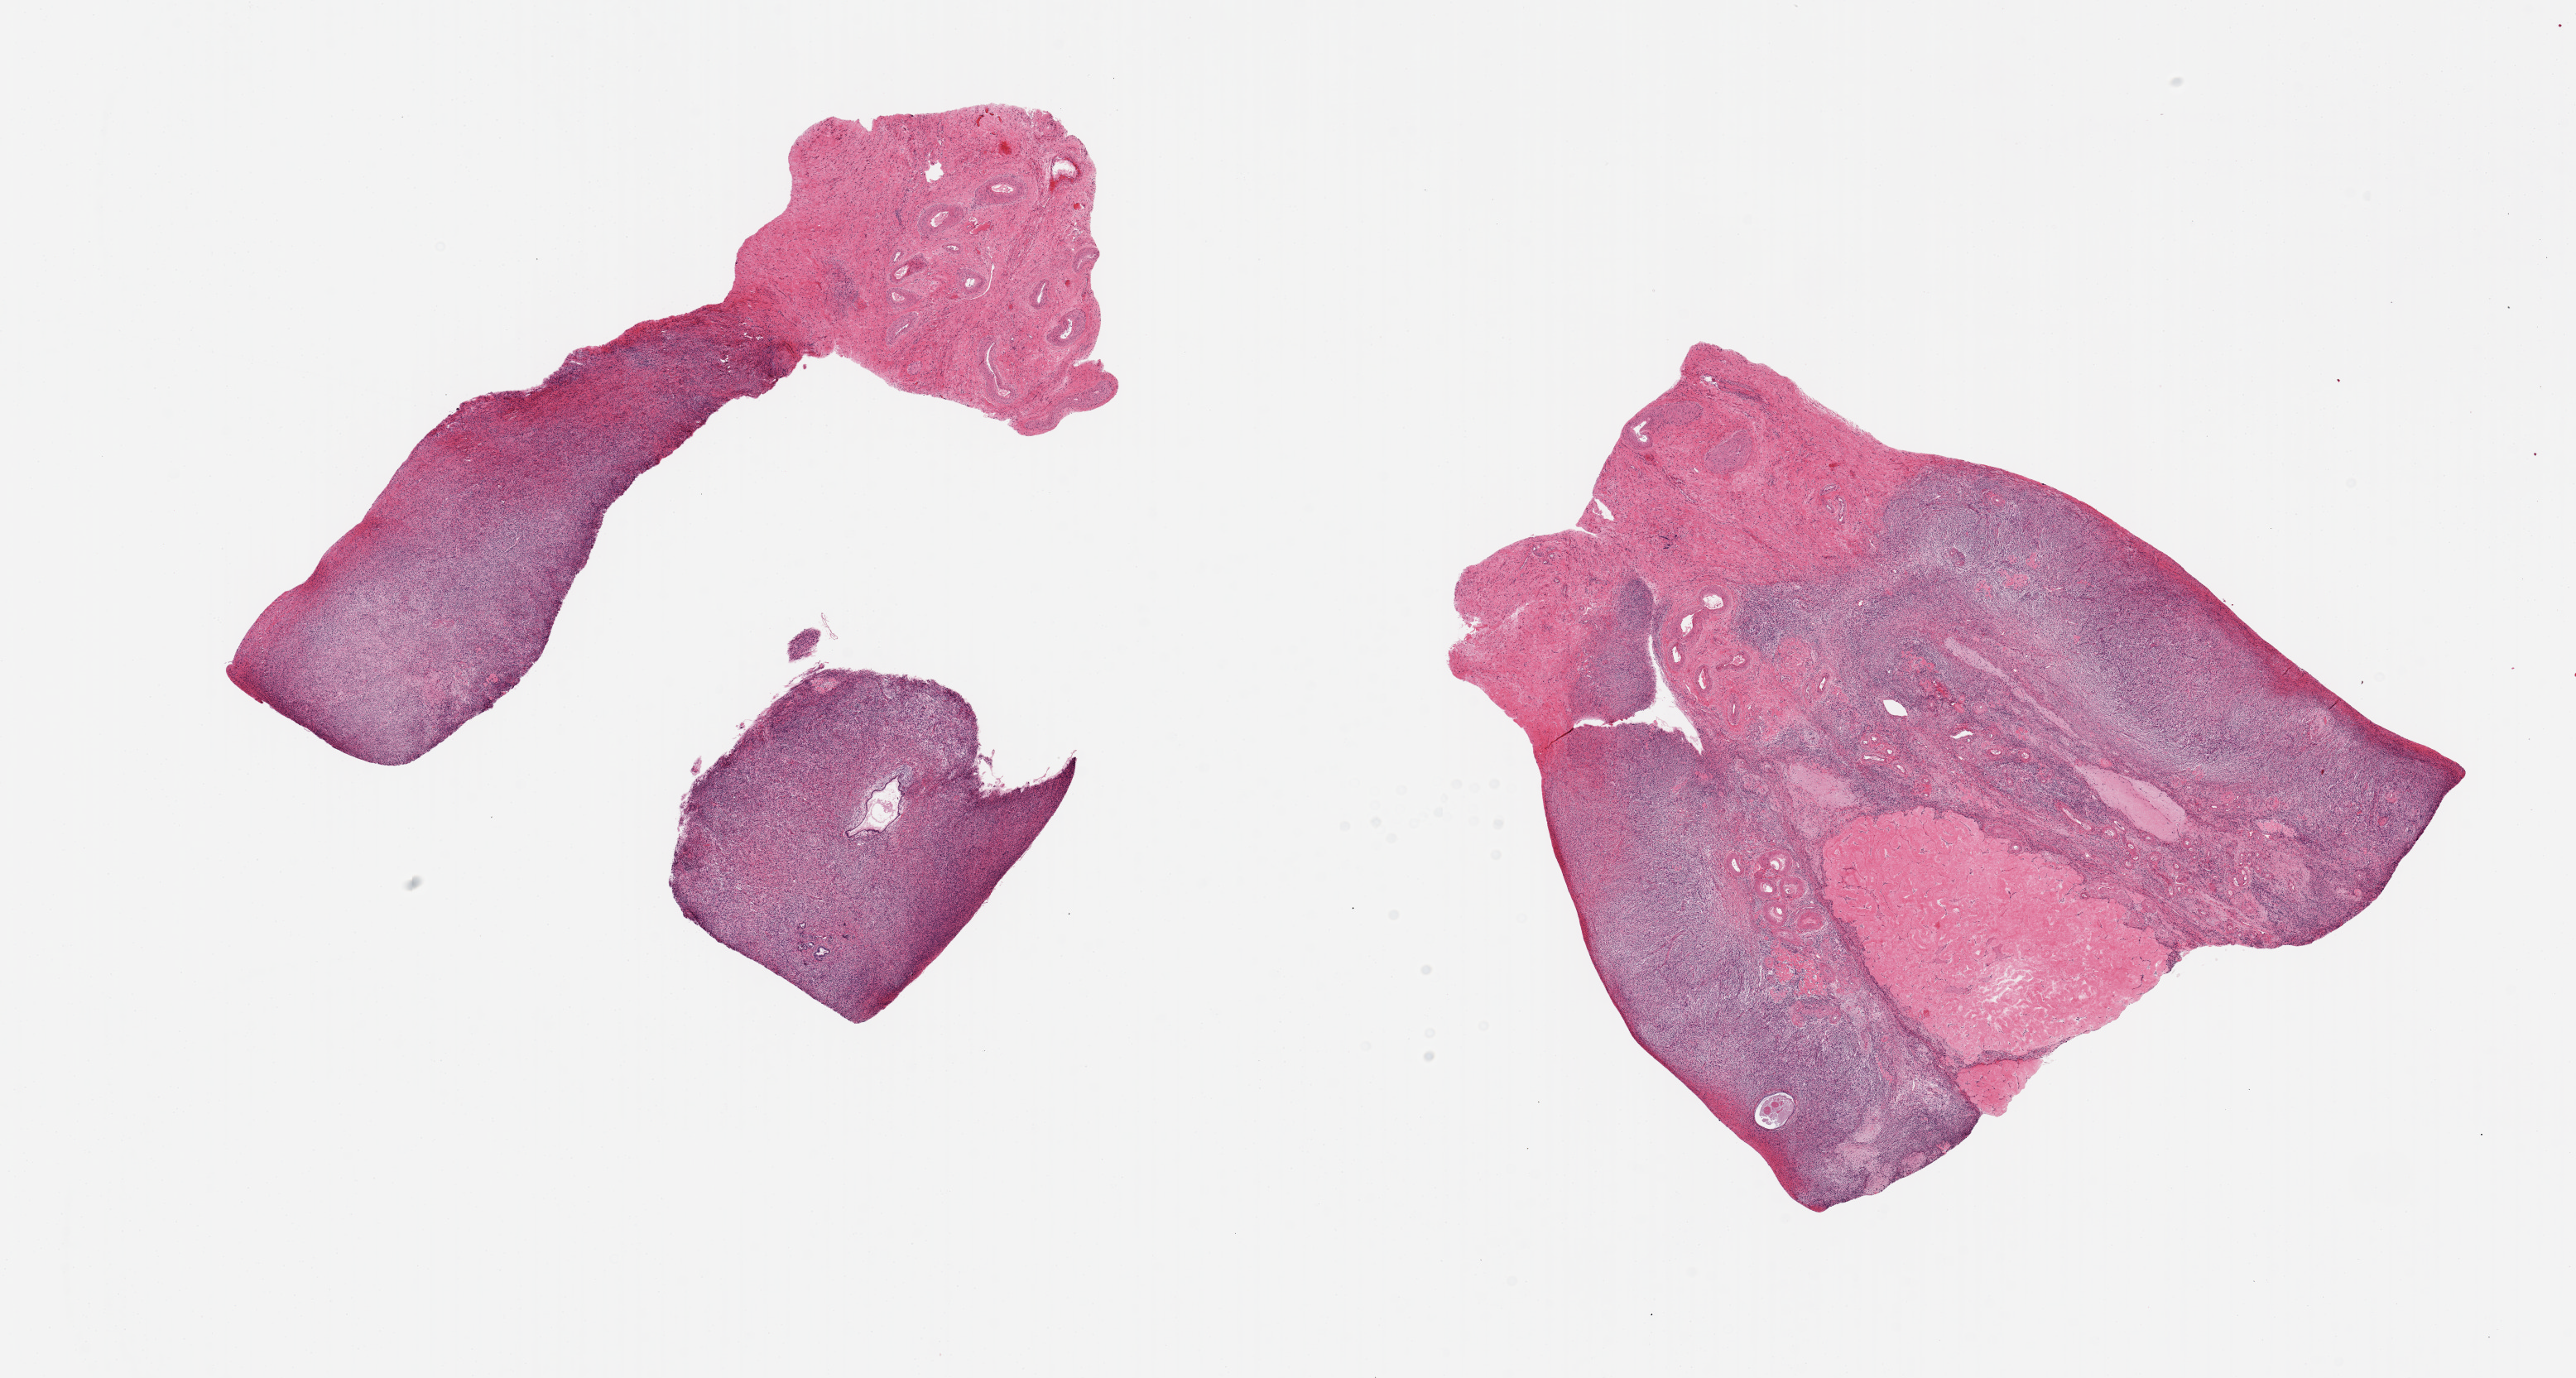
Digitized H&E-stained section, whole scanned area (about 24.6 x 13.2 mm) shown as a low-resolution overview, PAXgene-fixed, paraffin-embedded tissue, sampled site (target tissue): ovary, tissue donor sample. Donor sex: female.
• reviewer comment on this tissue sample: 2 pieces. 9x7 & 9x7.5mm; corpora albicans, no ova